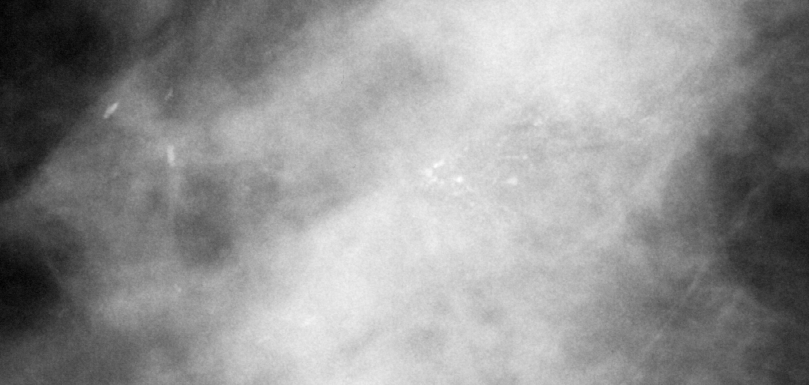
Region of interest cut from a scanned film mammogram (one marked finding), right breast, CC view, BI-RADS breast density category 3 (scale 1–4).
Calcifications, morphology fine linear branching, distribution segmental; BI-RADS assessment category 5; subtlety rating 4 on a 1 (subtle) to 5 (obvious) scale; pathology (as recorded): malignant.